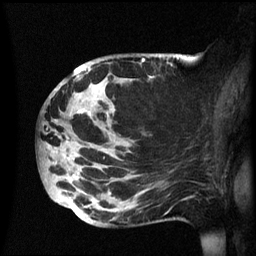
Breast MRI (dynamic contrast-enhanced), one sagittal slice. Position 32 of 60 along the scan axis. Dynamic contrast-enhanced series, image 2 of 3 at this slice position (ordered by acquisition). 1.5 T. TE 4.2 ms, TR 8.4 ms. 2.4 mm slice thickness. 256 × 256 image matrix, field of view 230 × 230 mm. Female patient, age 49 years.
Annotated regions visible in this slice (semi-automatic segmentation, software-assisted and operator-edited):
- analysis volume of interest (the breast-tissue region the enhancement analysis was run in; not a lesion): bounding box <39,54,174,227> (left, top, right, bottom; pixels)
- tumour enhancement mask (voxels above the 70 % enhancement threshold inside the analysis volume of interest): <77,60,152,218>